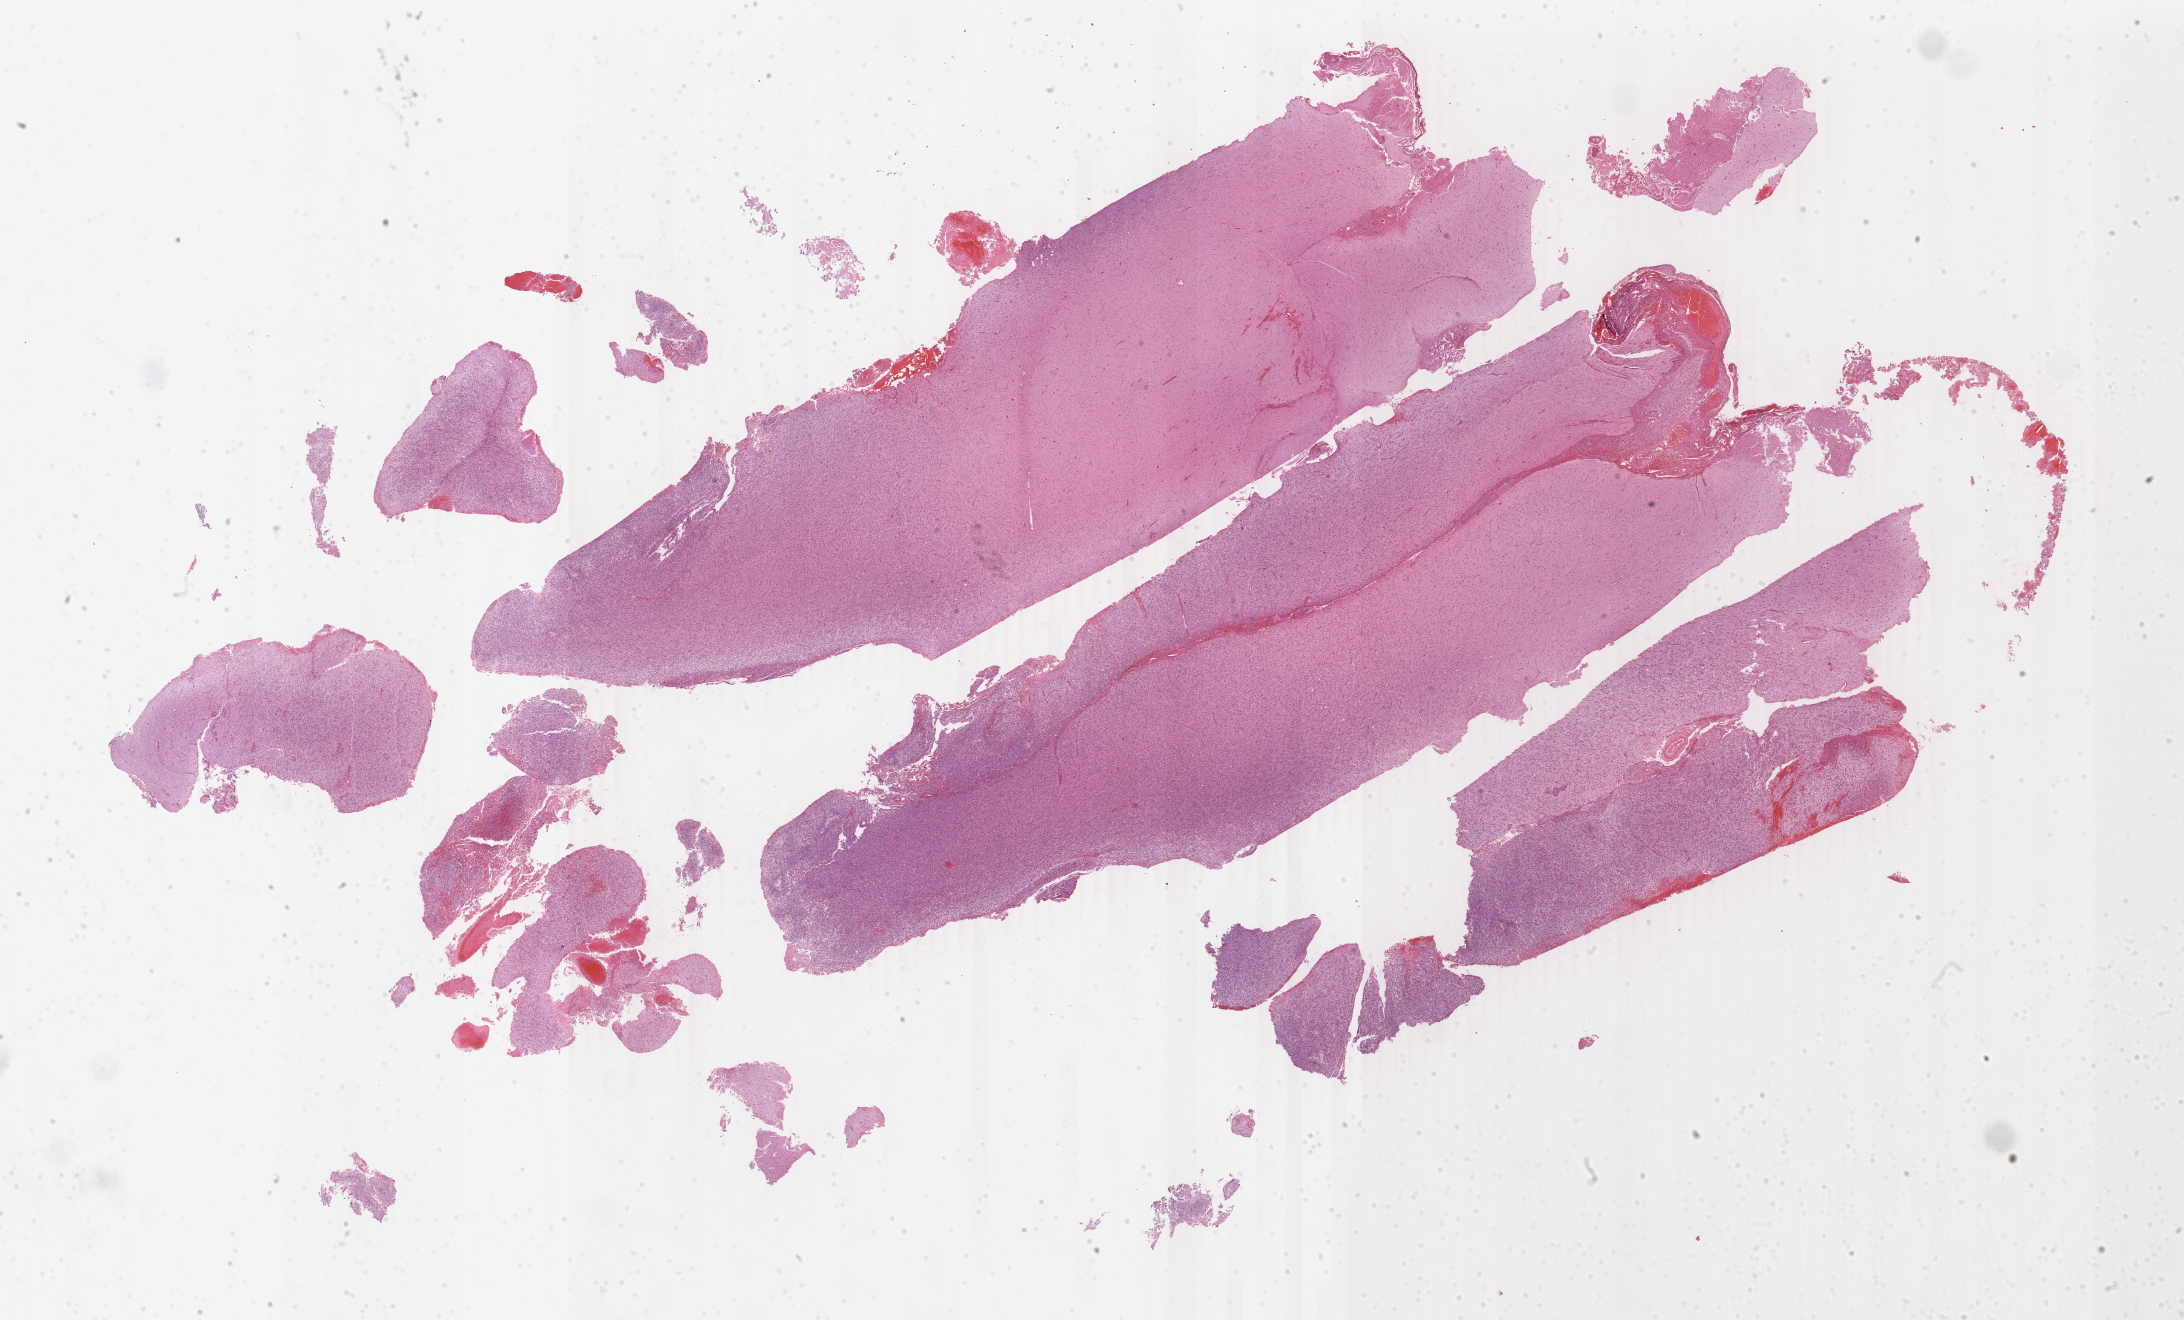
Whole-slide histology image, H&E-stained, whole scanned area (about 34.7 x 21.0 mm) shown as a low-resolution overview, FFPE section, primary tumour sample from the brain. Female, age 60 years at initial diagnosis.
* pathologic diagnosis: Glioblastoma